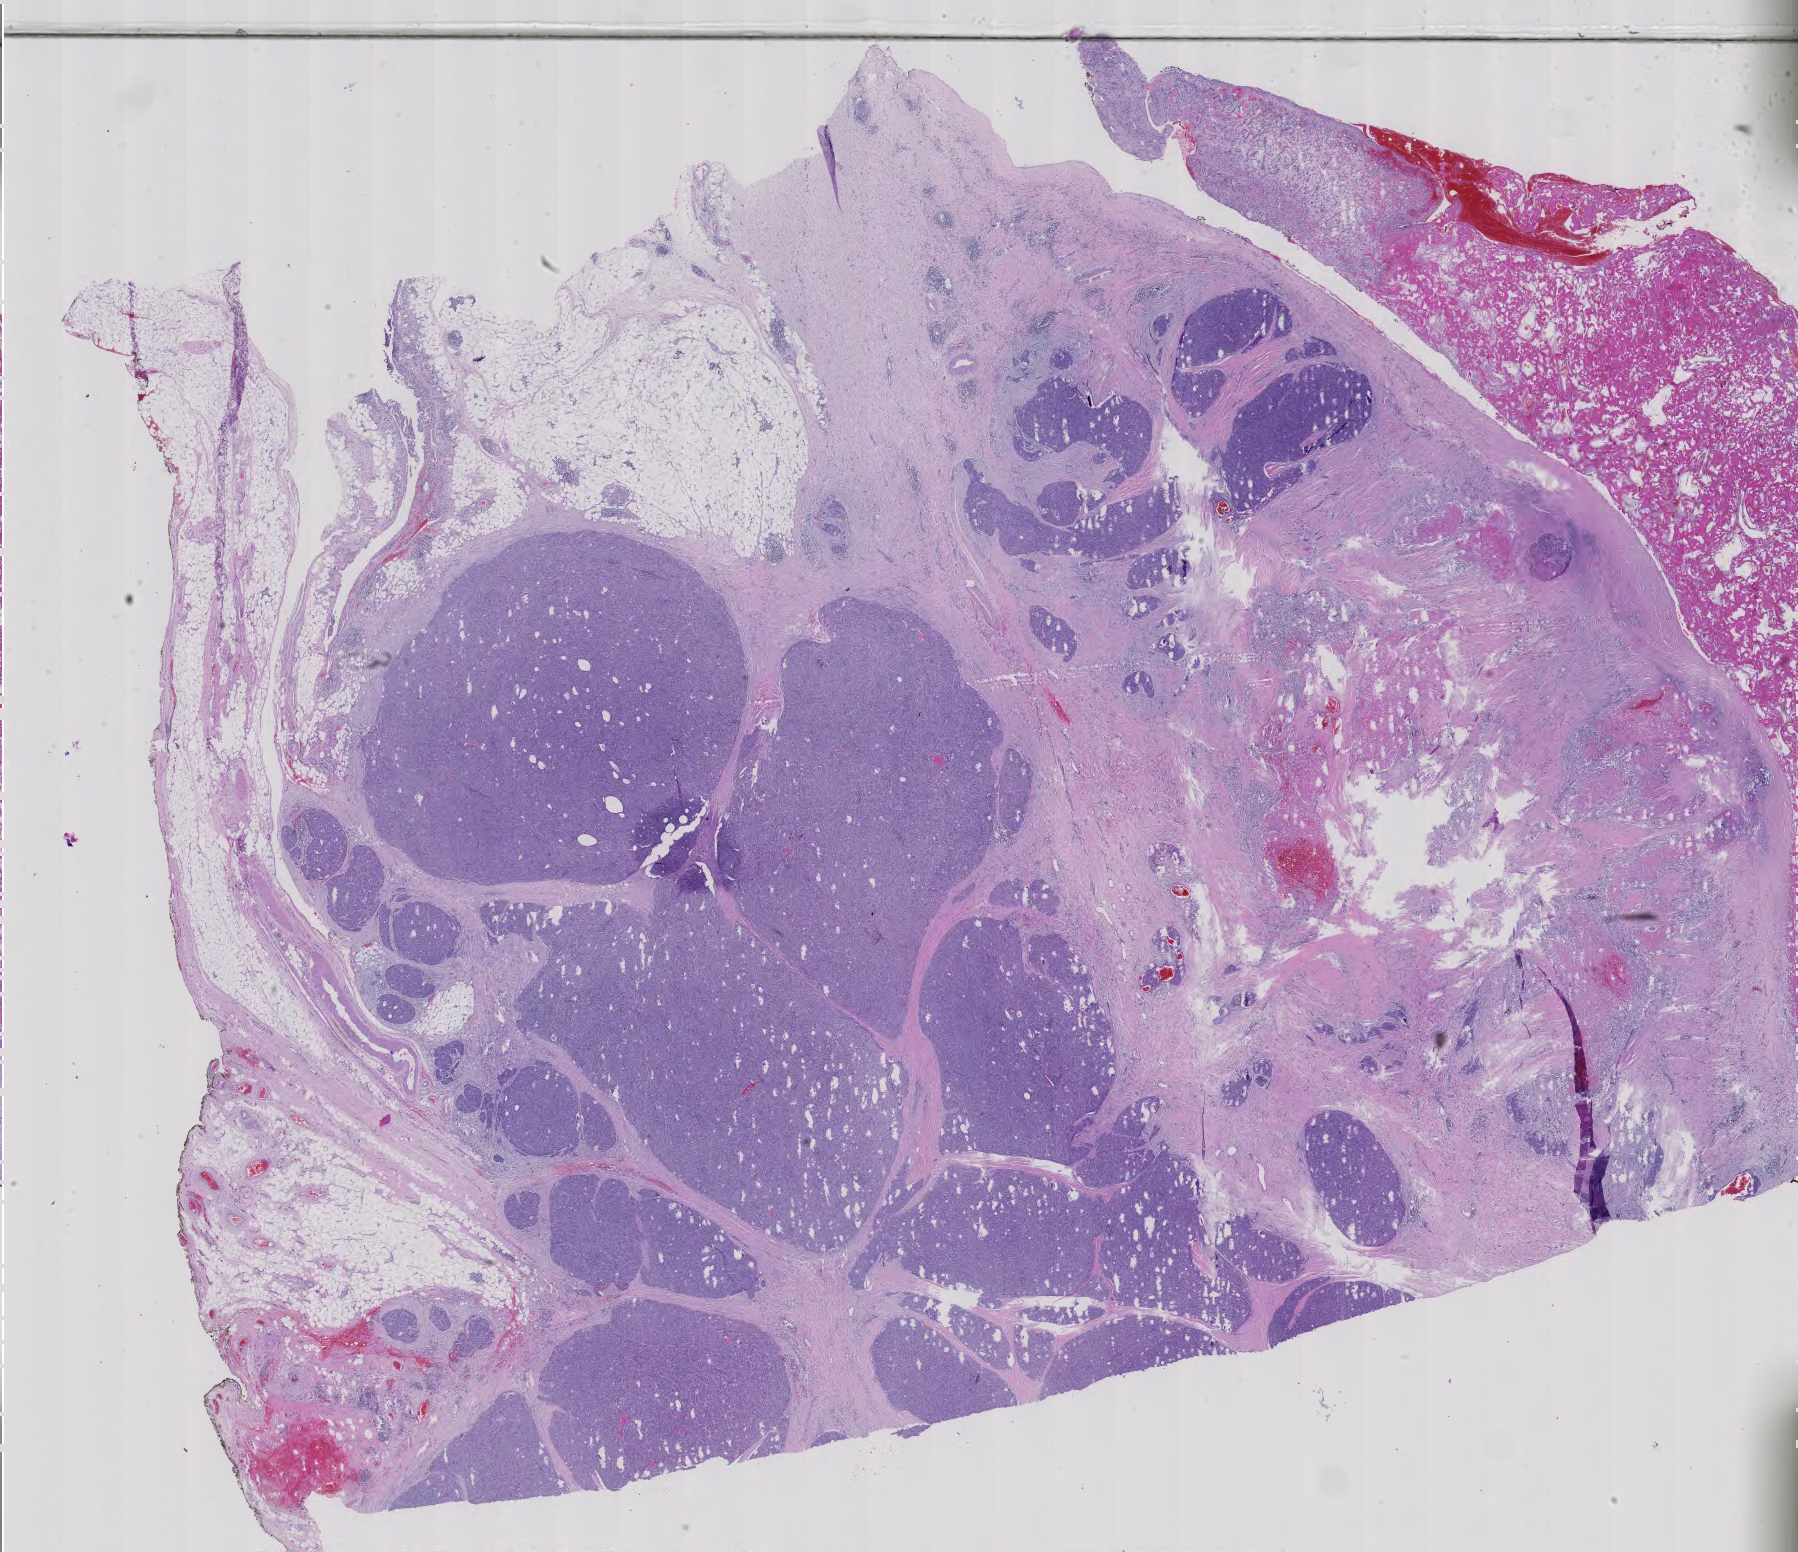
Whole-slide histology image, Hematoxylin and eosin (H&E) stained, a low-resolution overview of the entire scanned area, about 26.2 x 22.6 mm; FFPE section; thymus, primary tumour sample. Female, age 72 years at initial diagnosis.
• histologic diagnosis: Thymic carcinoma, NOS (anterior mediastinum)